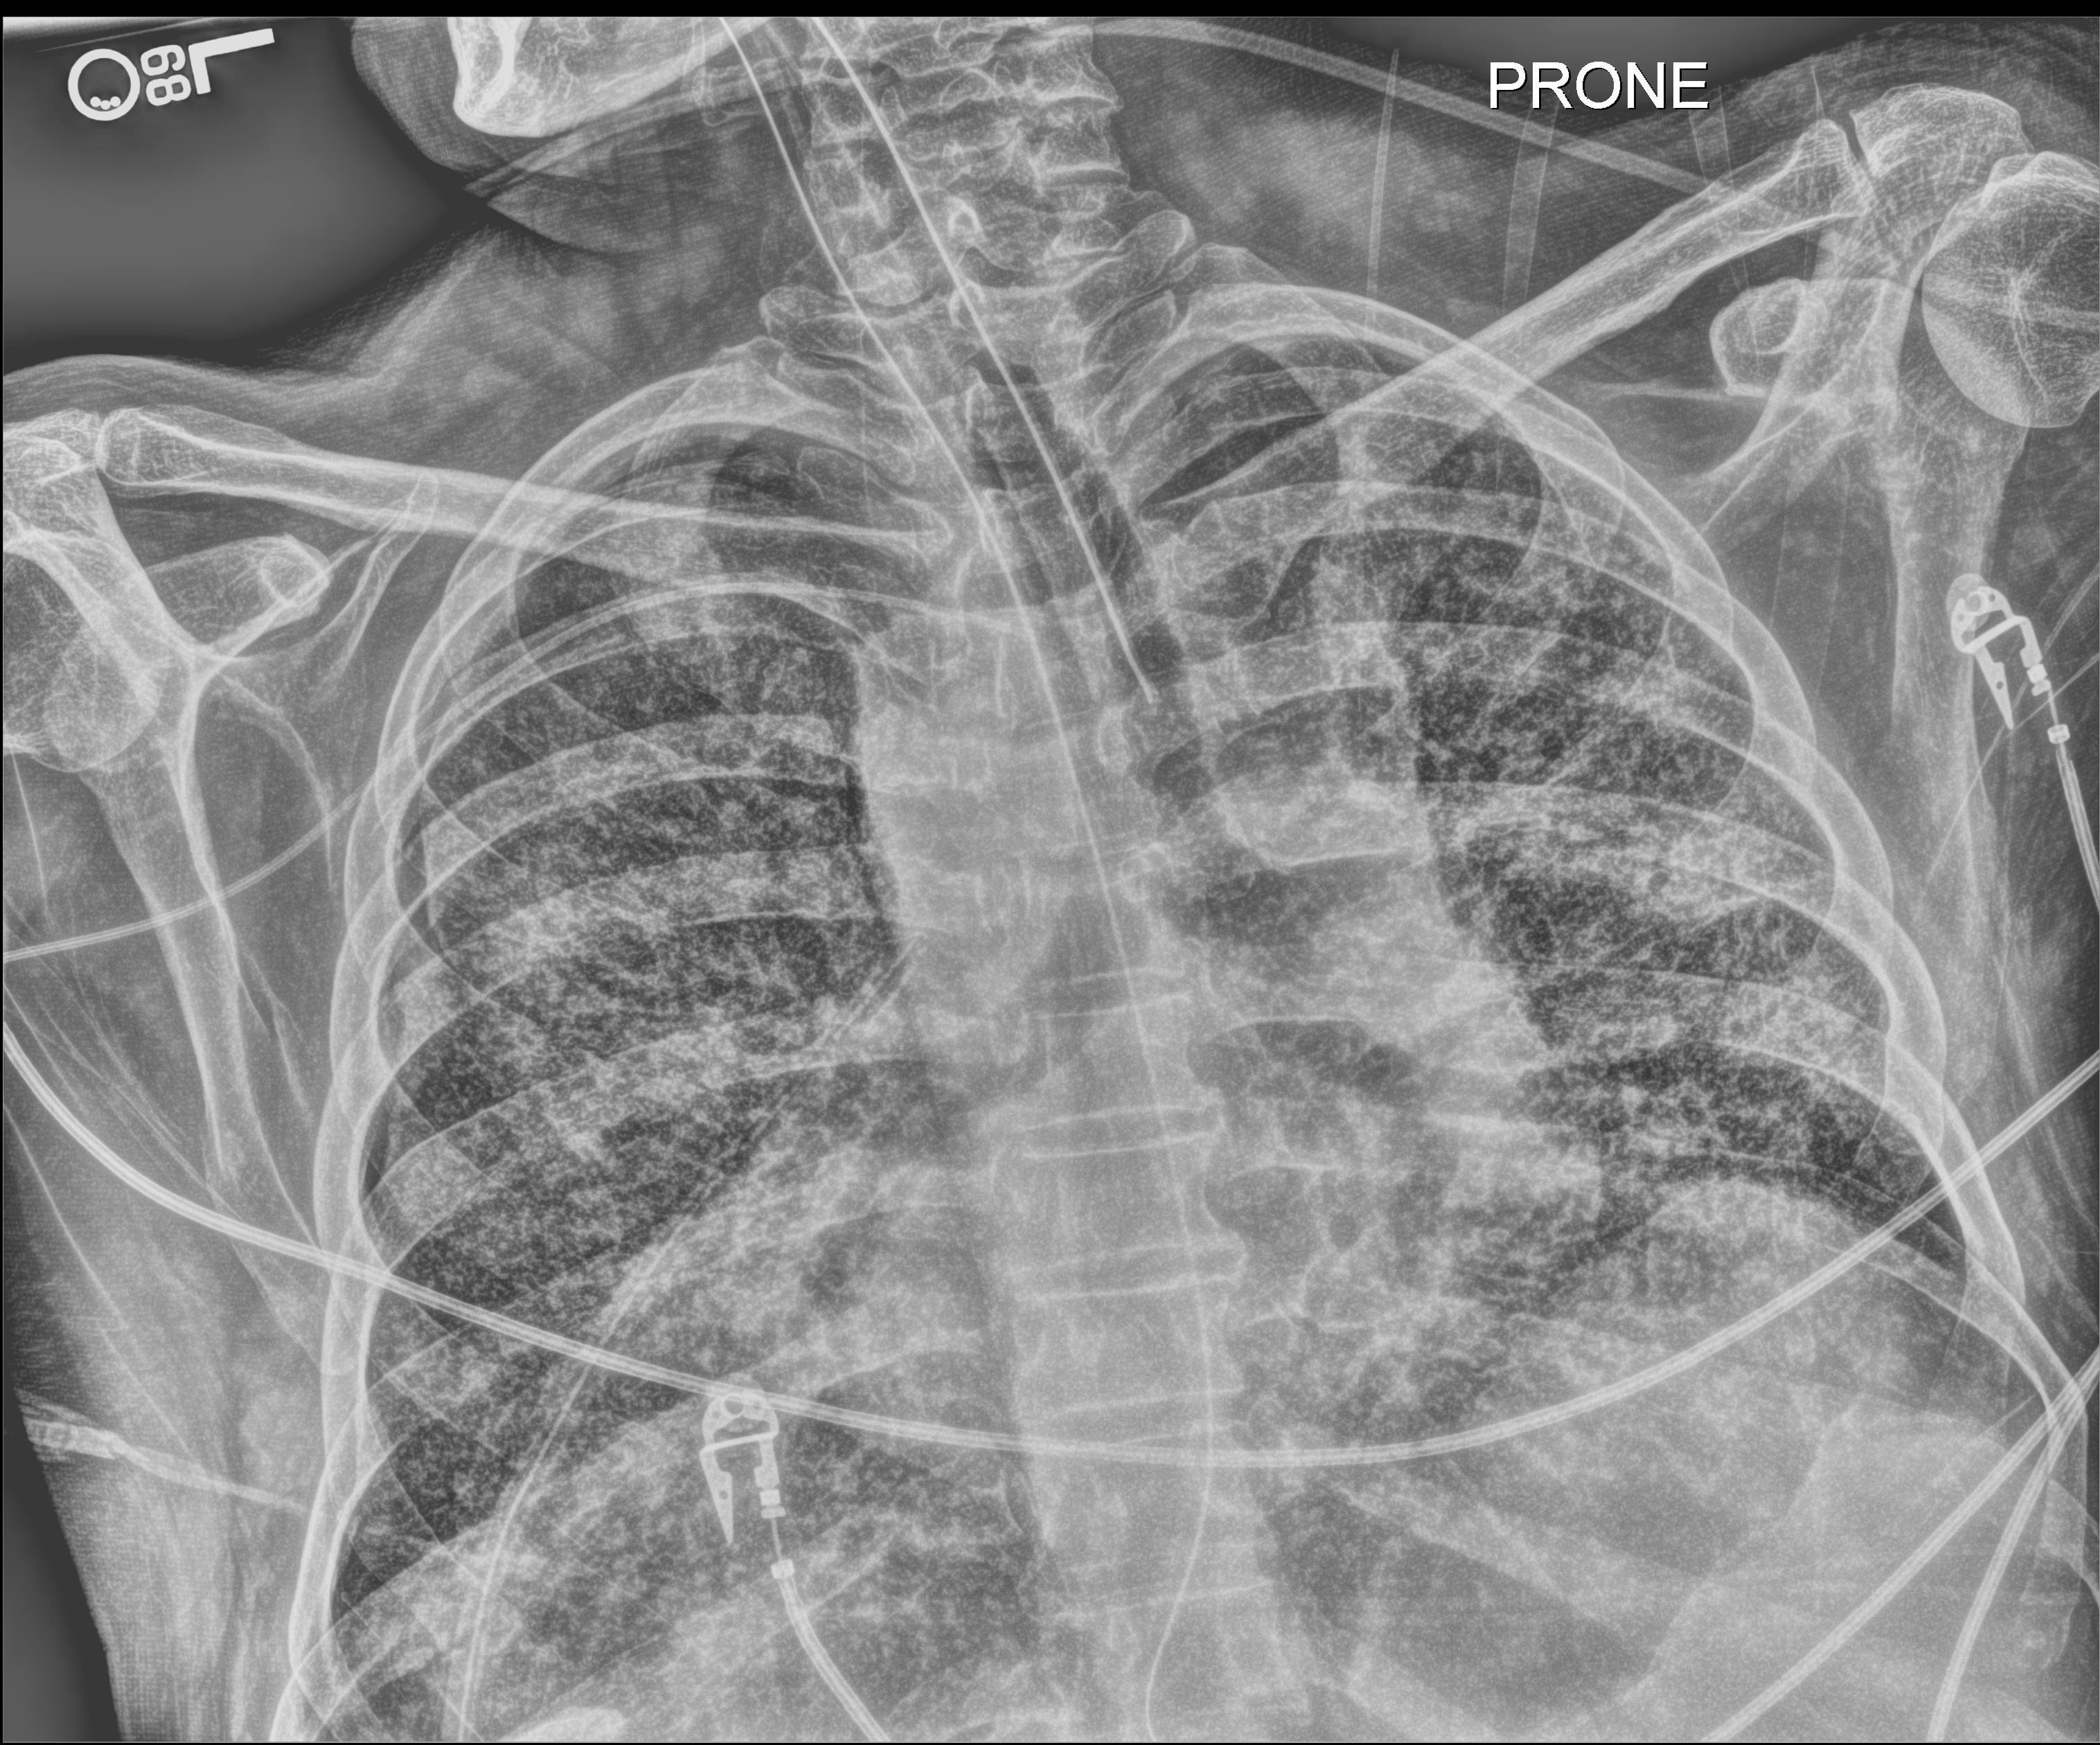
Chest radiograph, posteroanterior (PA) projection. Male patient hospitalised with COVID-19, age 60–74 years.
Hospital-stay facts (about this admission, not read from this image; timing relative to this image not recorded):
- mechanically ventilated during this hospital stay: yes